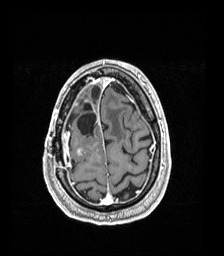
Brain MRI from a brain-tumour surgery series, one axial slice. Position 38 of 192 along the scan axis. T1-weighted post-contrast. 1 mm slice thickness. 224 × 256 image matrix, field of view 224 × 256 mm. From the clinical record (not read from this slice): histopathology: Astrocytoma; WHO grade: 4; IDH mutation: yes; tumour location: Right Frontal.
Outlined on this slice (expert manual segmentation):
- previous resection cavity: bounding box [x1, y1, x2, y2] px = [77, 104, 96, 135]
- tumour: [77, 145, 84, 156]